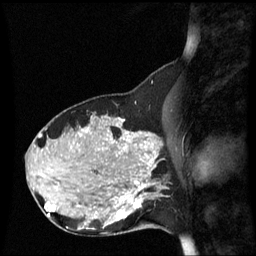
Breast MRI (dynamic contrast-enhanced), one sagittal slice. Position 24 of 60 along the scan axis. Dynamic contrast-enhanced series, image 2 of 3 at this slice position (ordered by acquisition). 1.5 T. TE 4.2 ms, TR 8.9 ms. 2.2 mm slice thickness. 256 × 256 image matrix, field of view 220 × 220 mm. Patient: female, 31 years. From the clinical record (not read from this slice): setting: breast cancer imaged before/during neoadjuvant chemotherapy; receptor status: HR-positive, HER2-negative.
Annotated regions visible in this slice (semi-automatically segmented with operator editing):
- analysis volume of interest (the breast-tissue region the enhancement analysis was run in; not a lesion): bounding box <90,180,152,235> (left, top, right, bottom; pixels)
- tumour enhancement mask (voxels above the 70 % enhancement threshold inside the analysis volume of interest): <118,180,148,221>